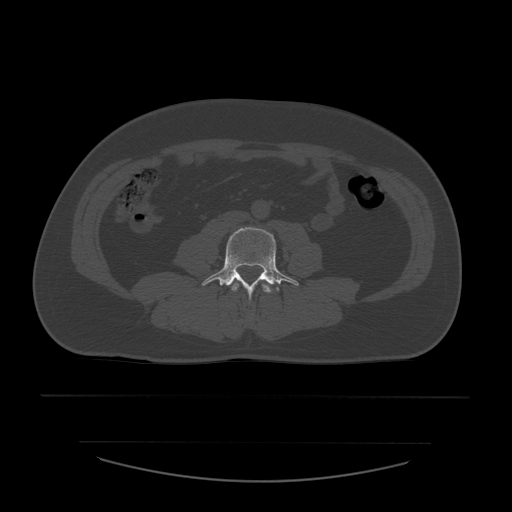
CT including the spine, one axial slice. Position 152 of 532 along the scan axis. Reconstruction kernel STANDARD. Bone window (W 1800 / L 400 HU). 512 × 512 image matrix, field of view 441 × 441 mm. Patient age 44 years. Case-level facts recorded for this patient, not image findings: primary cancer: soft tissue sarcoma.
Annotated regions visible in this slice (semi-automatically segmented with operator editing):
- L3 vertebra: bounding box <232,282,273,293> (left, top, right, bottom; pixels)
- L4 vertebra: <201,227,299,298>